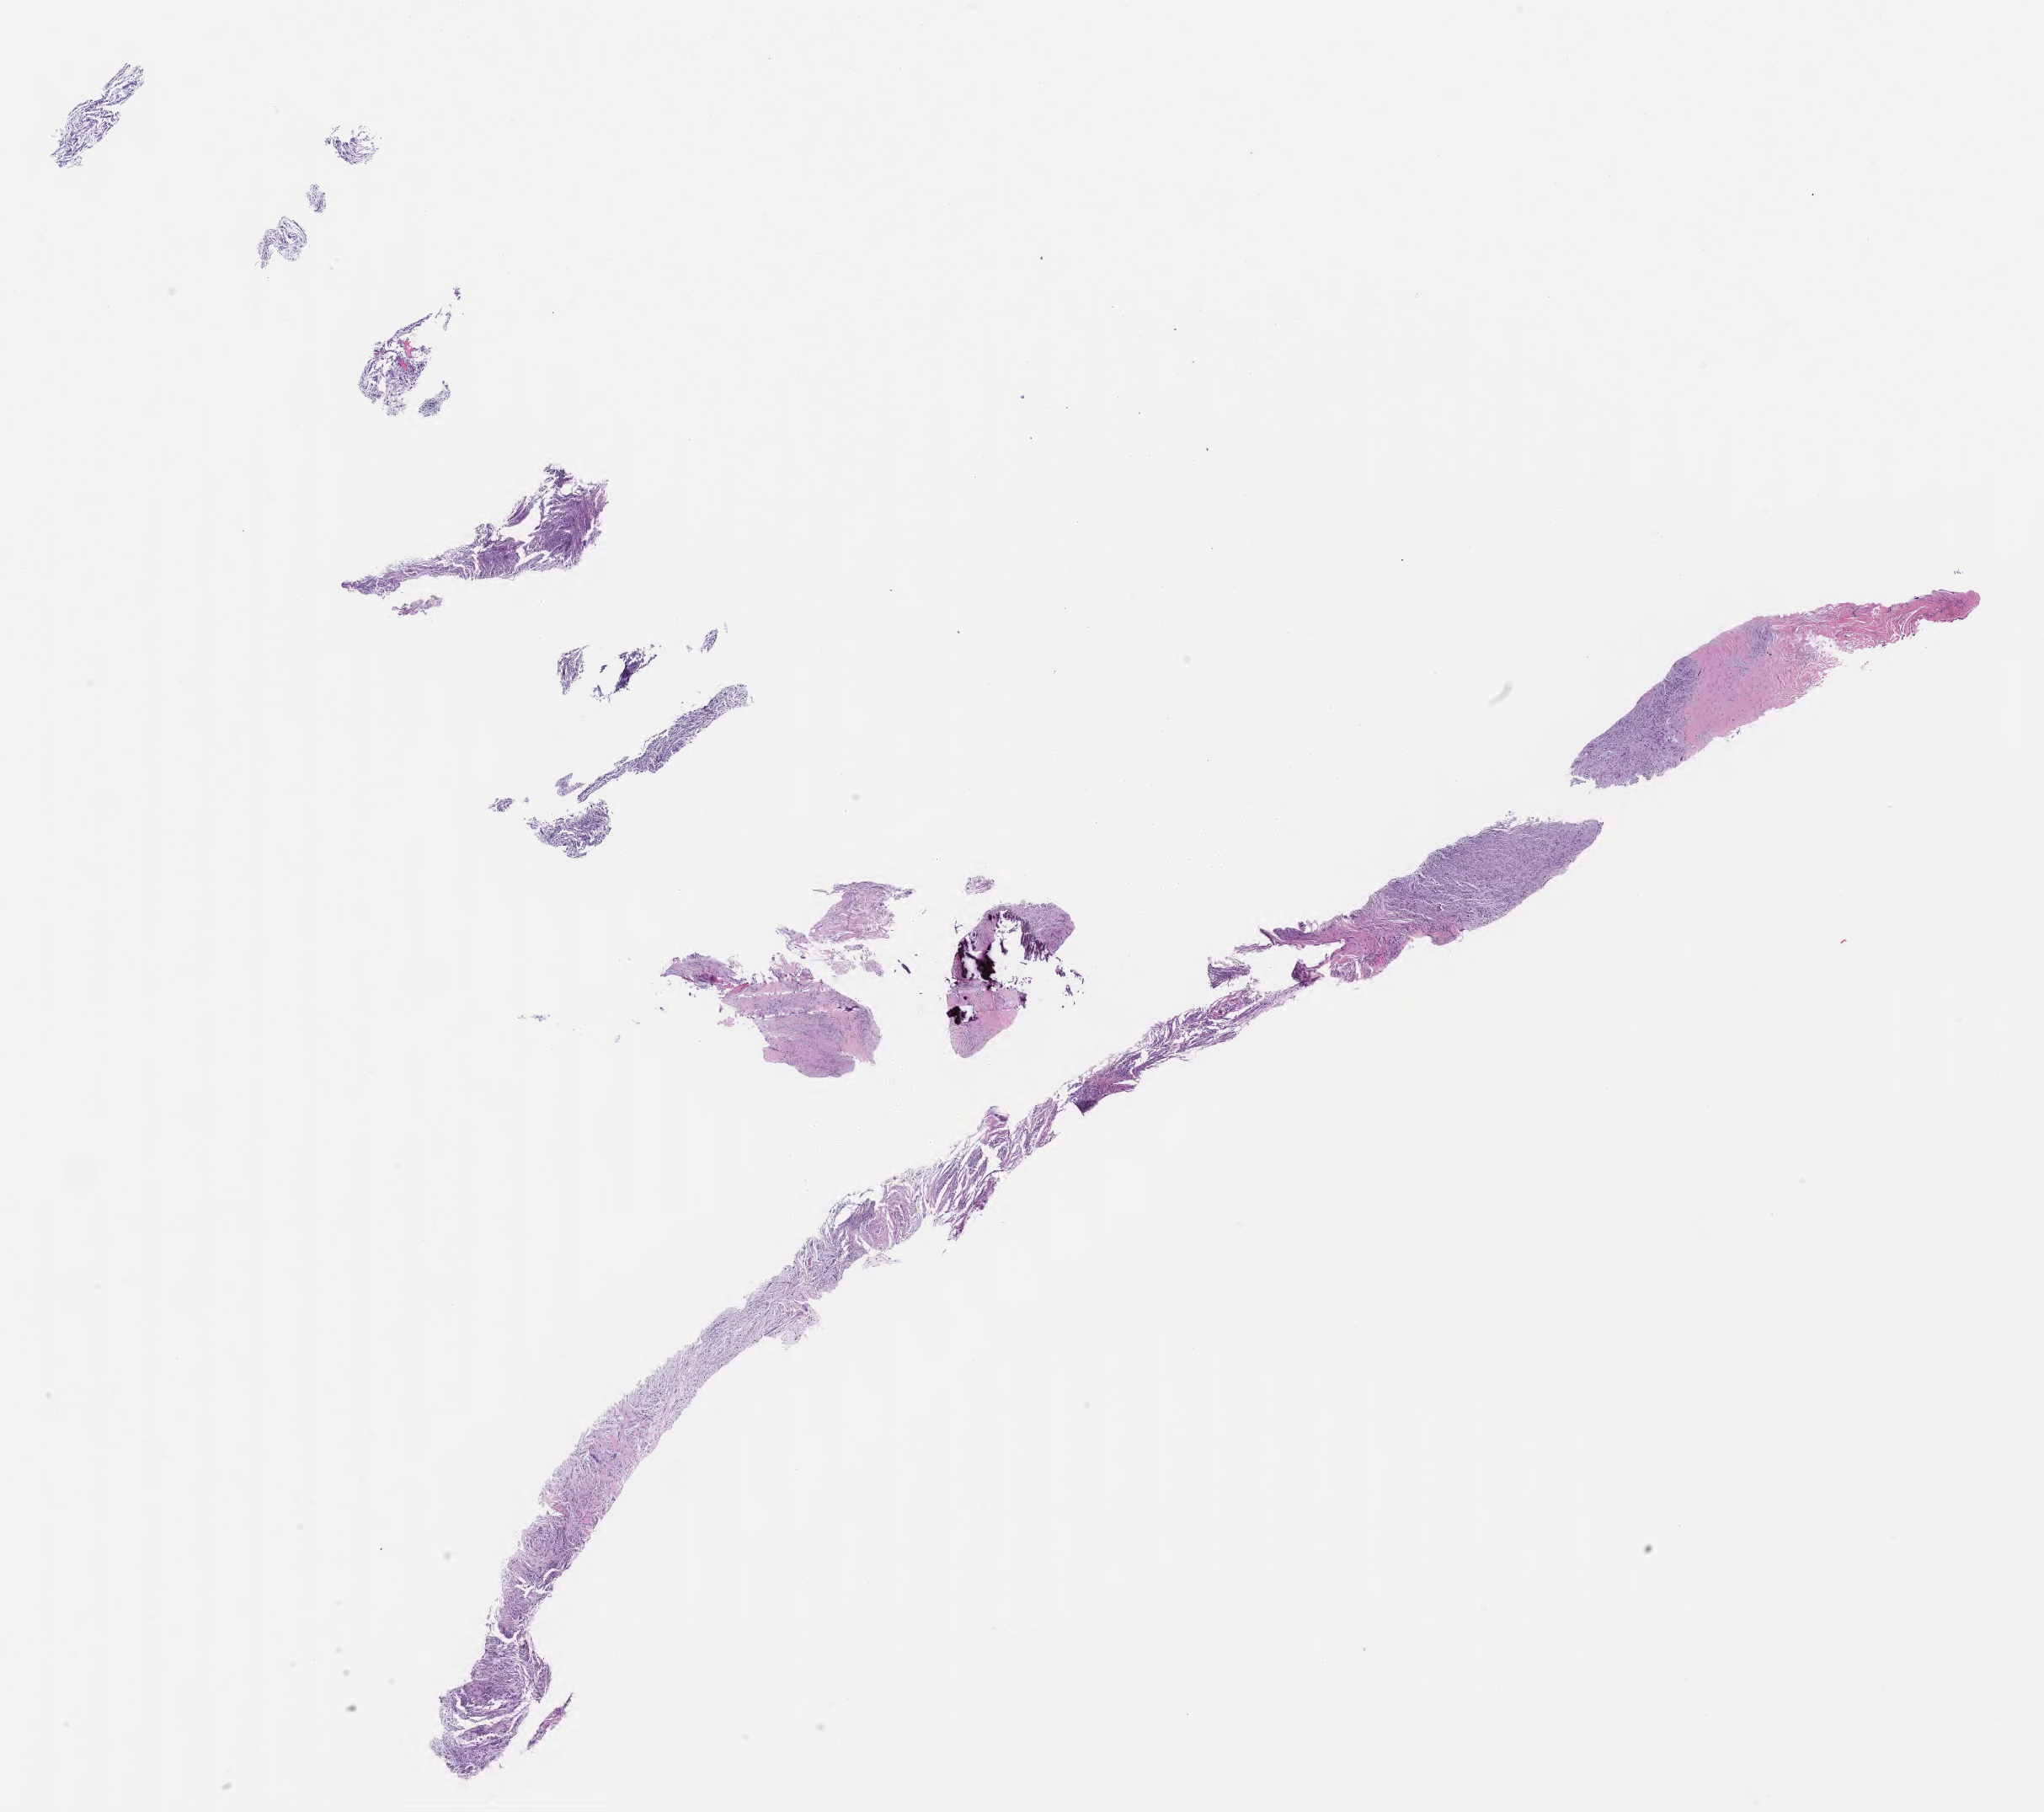
Whole-slide image, H&E stain of tumor tissue from the abdomen, a low-resolution overview of the entire scanned area, about 19.6 x 17.4 mm. Formalin-fixed, paraffin-embedded (FFPE) tissue. Patient: female, age 60 months (5 years).
Recorded diagnosis: Myofibroblastic tumor, NOS.